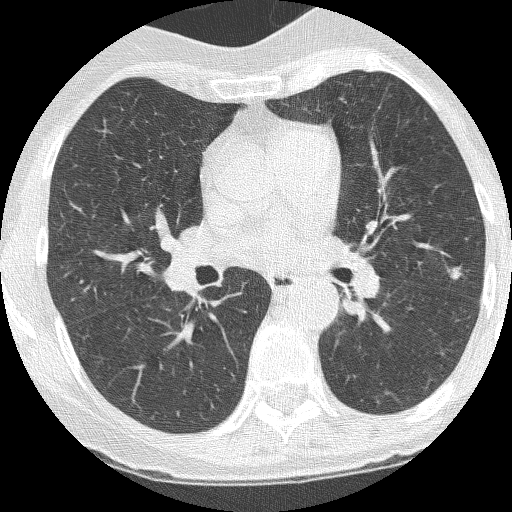
Low-dose screening chest CT, axial slice; third screening round (two years after baseline); lung window (W 1500 / L -600 HU); 120 kVp. Female, age 60 years at enrolment. Current smoker at enrolment.
• Lesion marked by an expert reader, bounding box [x1, y1, x2, y2] px = [436, 260, 472, 292].
• The screening reader recorded 2 non-calcified nodules or masses ≥4 mm on this exam (left upper lobe, left upper lobe); which of them this box marks is not recorded.
• Lung cancer was diagnosed 37 days after this screen: adenocarcinoma, NOS, left upper lobe, moderately differentiated (G2), stage IA (AJCC 6th edition), 6 mm at pathology.